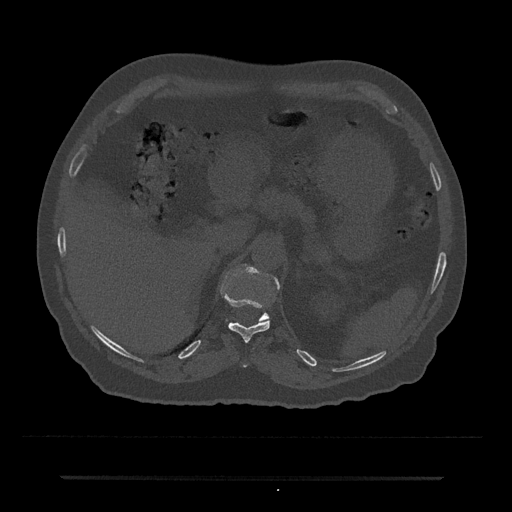
CT including the spine, one axial slice; slice 170 of 797 in the series (ordered by position); 120 kVp; bone window (W 1800 / L 400 HU); 512 × 512 image matrix, field of view 437 × 437 mm. Male patient, age 69 years. Case-level facts recorded for this patient, not image findings: primary cancer: prostate.
Structures marked on this image (semi-automatically segmented with operator editing):
- T10 vertebra: bounding box (x1, y1, x2, y2) in pixels: (243, 365, 247, 368)
- T11 vertebra: (223, 294, 270, 342)
- T12 vertebra: (241, 268, 280, 321)